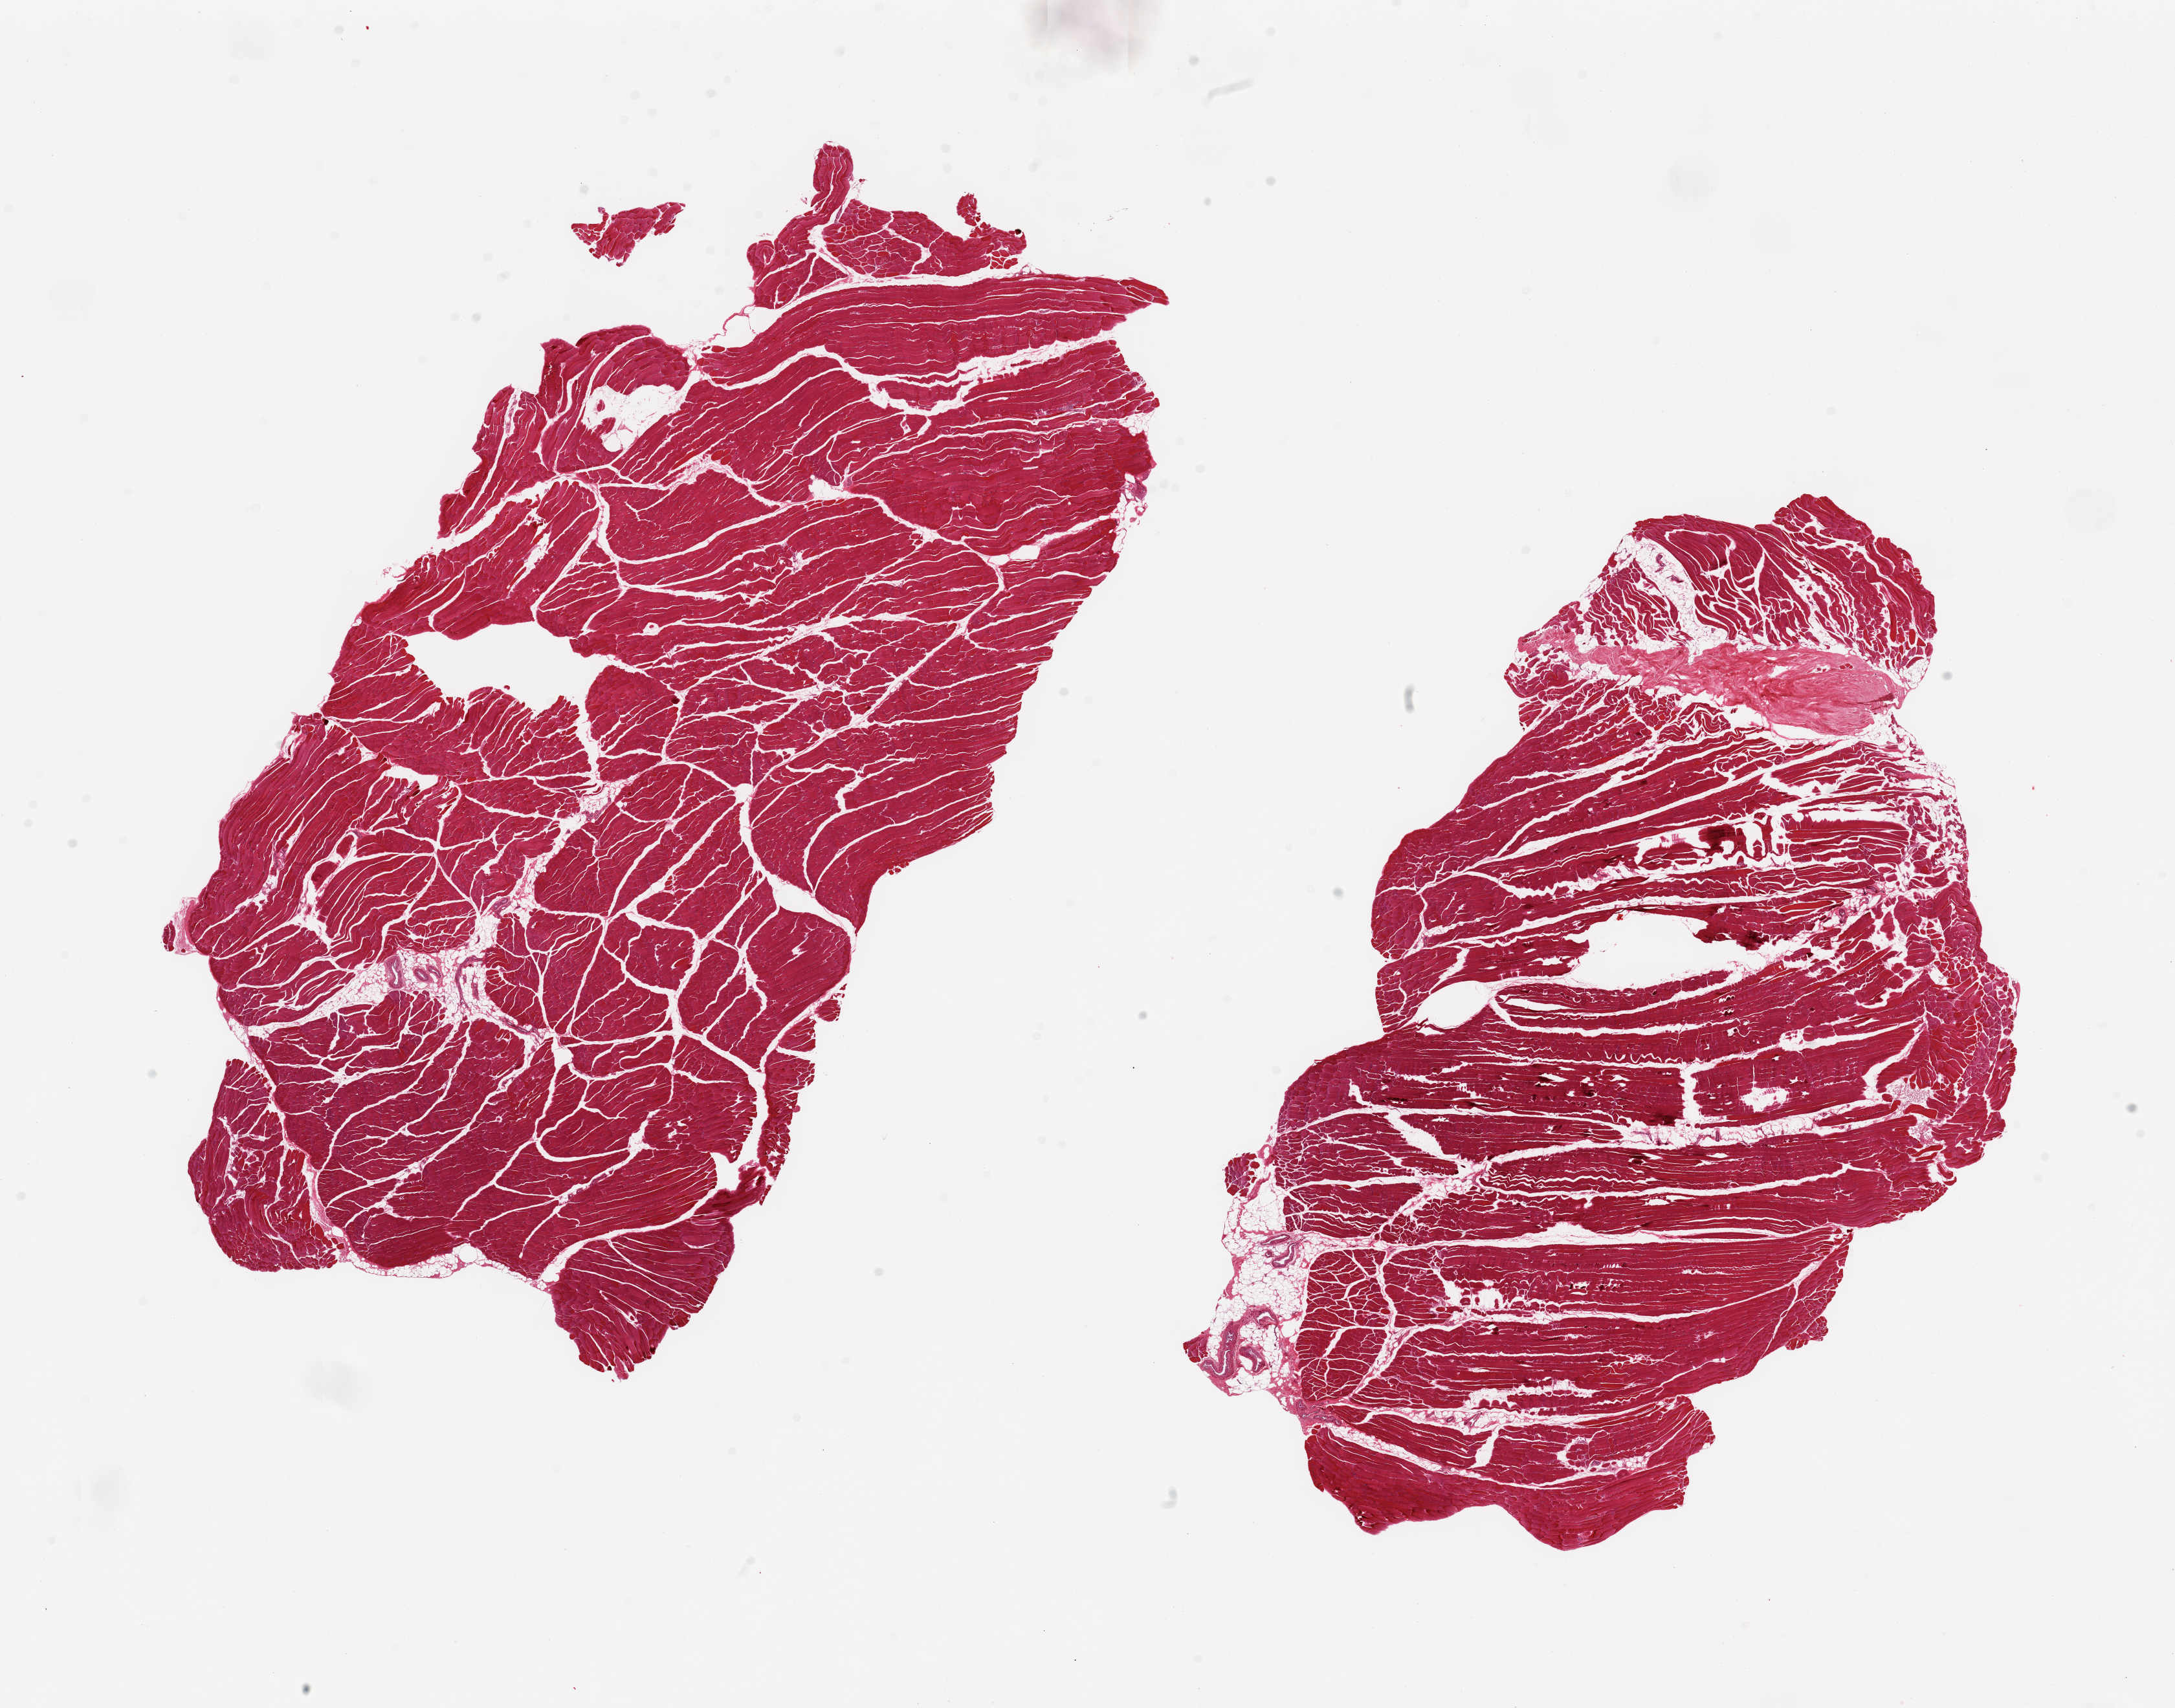
Hematoxylin and eosin (H&E) whole-slide image, low-resolution overview of the scanned area, about 26.6 x 20.9 mm (slide scanned at 20x). PAXgene-fixed, paraffin-embedded tissue. Target tissue: skeletal muscle. Tissue donor sample. Donor sex: female.
- reviewer comment on this tissue sample: 2 pieces